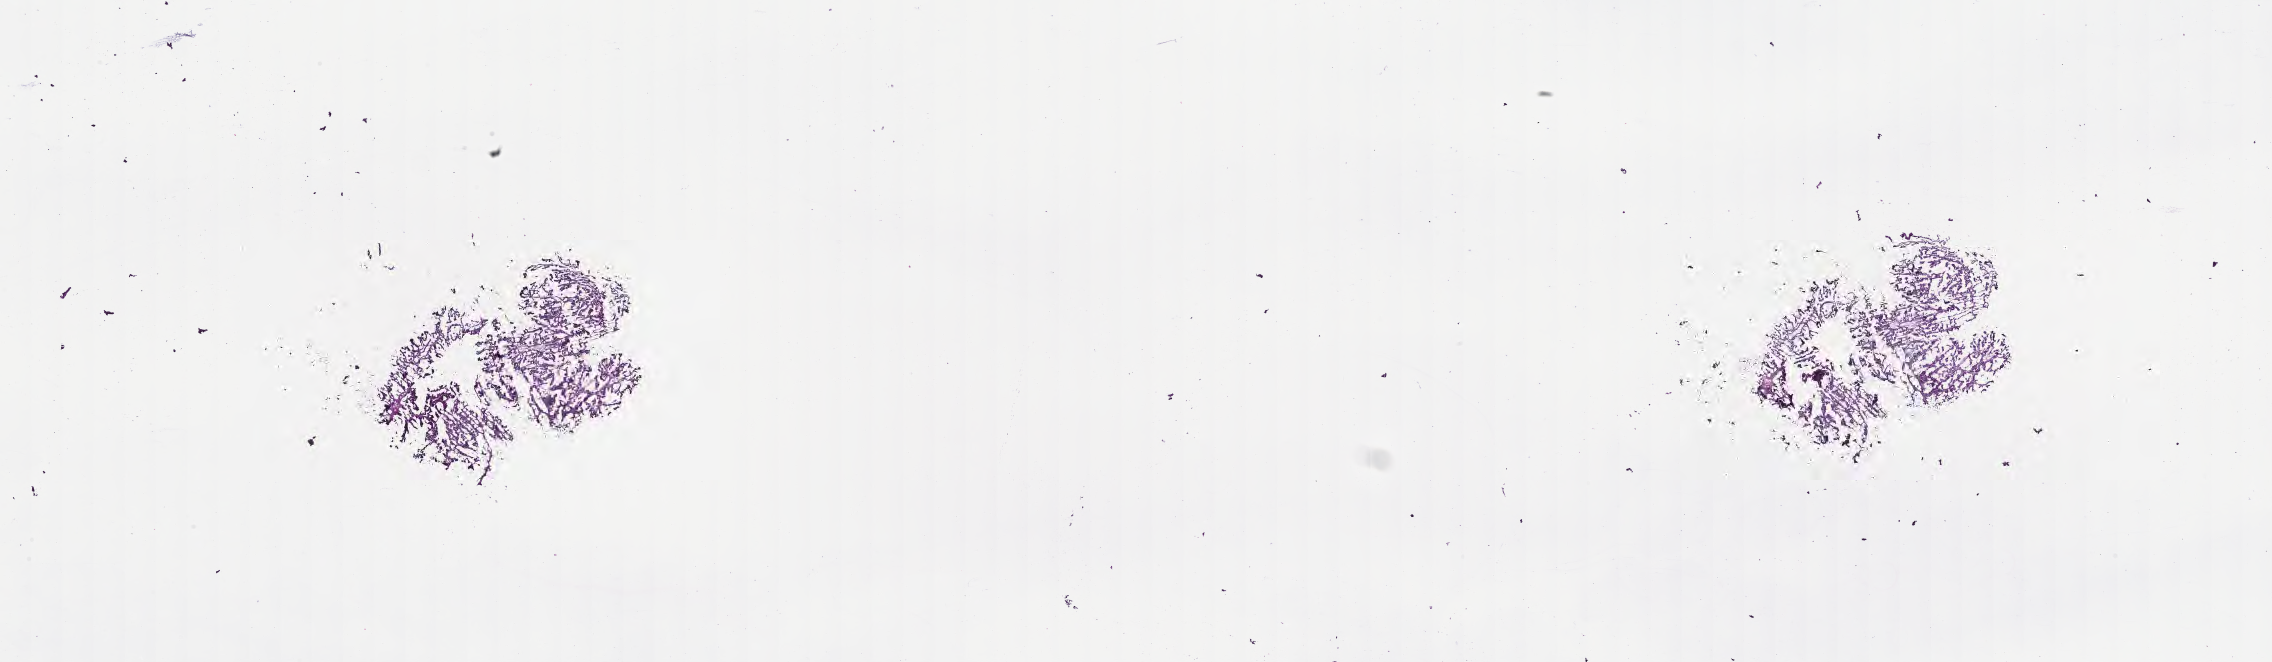
Haematoxylin and eosin whole-slide image of tumor tissue from the brain — a low-resolution overview of the entire scanned area, about 36.7 x 10.7 mm, frozen section (OCT-embedded). Male patient, age 257 days.
- diagnosis: Atypical choroid plexus papilloma